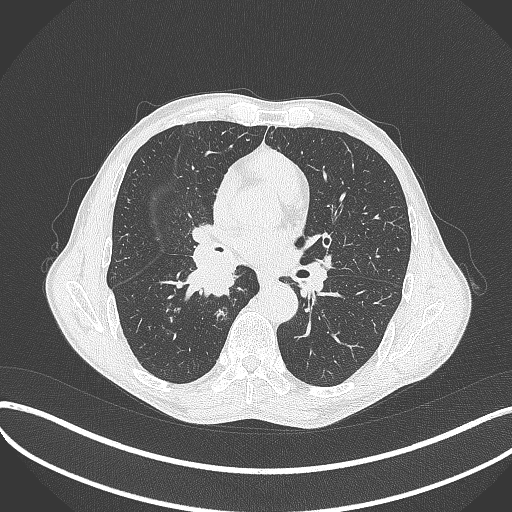
Chest CT, one axial slice; reconstruction kernel B70f; lung window (W 1500 / L -600 HU); 1 mm slice thickness; 512 × 512 image matrix. Male patient, age 65 years. From the clinical record (not read from this slice): clinical TNM (as recorded): T2a N0 M0; histopathological grade: G2.
Structures marked on this image (bounding box drawn by a radiologist):
- lung tumour (recorded histology: squamous cell carcinoma): bounding box [x1, y1, x2, y2] px = [171, 231, 241, 303]